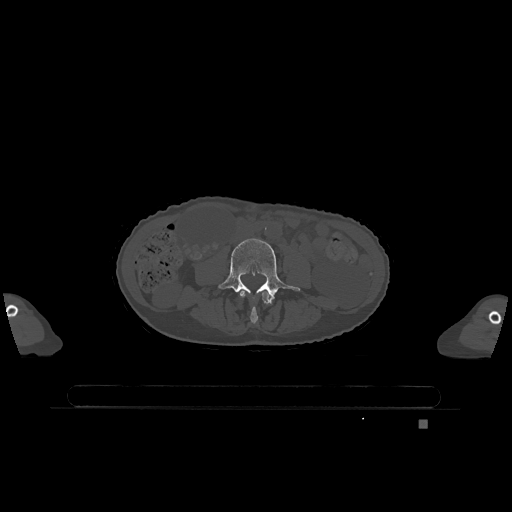
CT including the spine, one axial slice; slice 308 of 1317 in the series (ordered by position); bone window (W 1800 / L 400 HU); 0.5 mm slice thickness; 512 × 512 image matrix, field of view 500 × 500 mm. Female patient, age 74 years. From the clinical record (not read from this slice): primary cancer: lung; vertebrae with lytic lesions (as recorded): T1, T4, T5, T6, L4, L5.
Structures marked on this image (semi-automatic segmentation, software-assisted and operator-edited):
- L3 vertebra: bounding box [x1, y1, x2, y2] px = [240, 290, 272, 324]
- L4 vertebra: [218, 238, 300, 302]